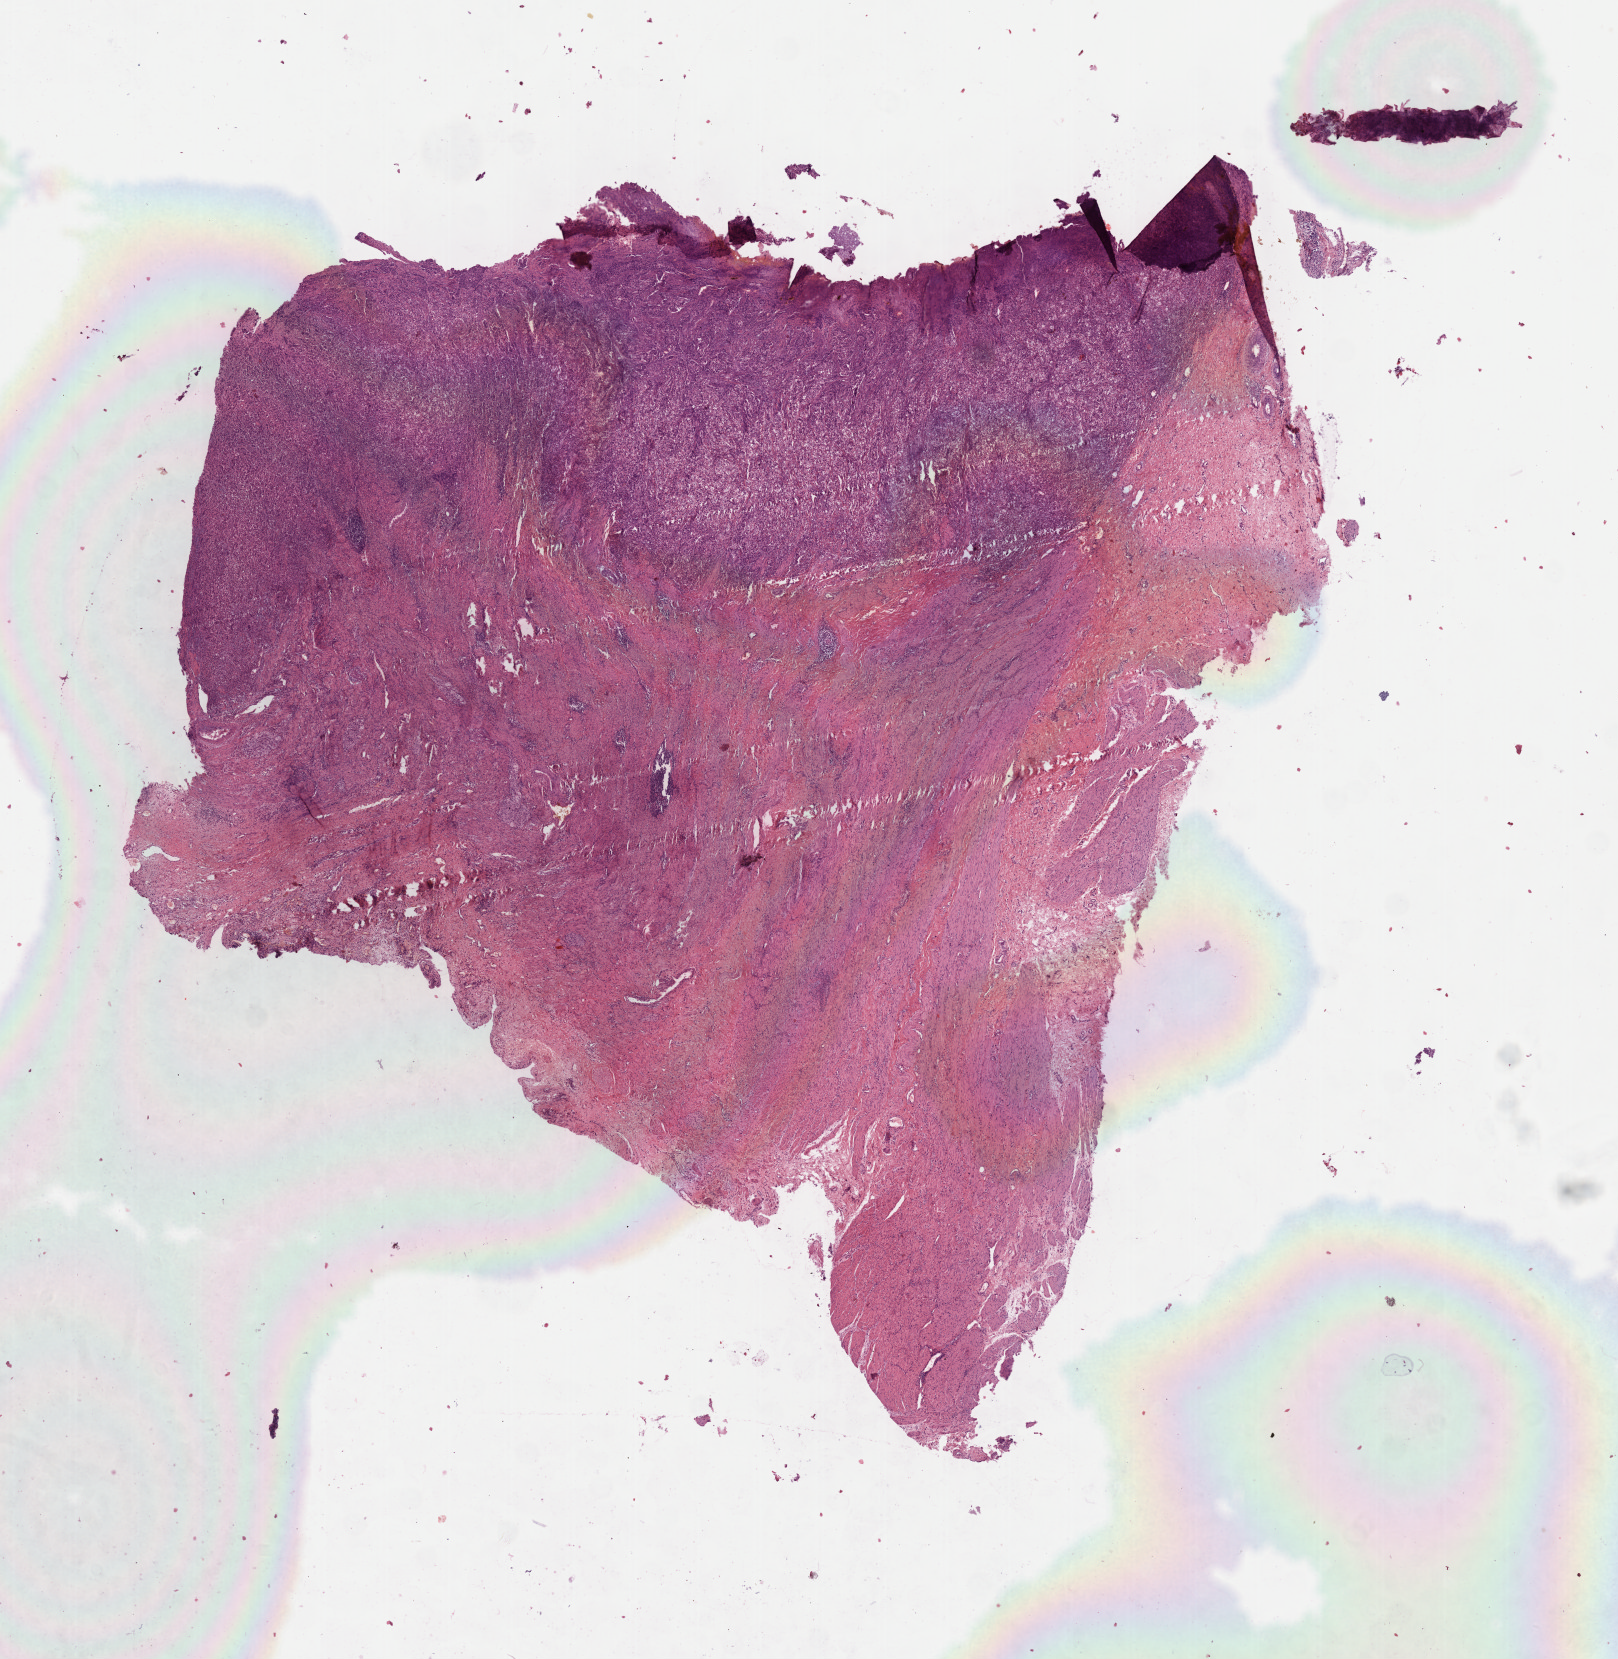
Whole-slide histology image, Hematoxylin and eosin (H&E) stained, shown as a low-resolution overview of the whole scanned area (about 13.1 x 13.4 mm, acquisition: 40x scan); formalin-fixed paraffin-embedded (FFPE) diagnostic section; primary tumour sample from the stomach. Patient: female, age at initial diagnosis 61 years. Histologic grade: GX (grade cannot be assessed).
AJCC pathologic stage: IB (7th edition). Diagnosis: Signet ring cell carcinoma (gastric antrum).